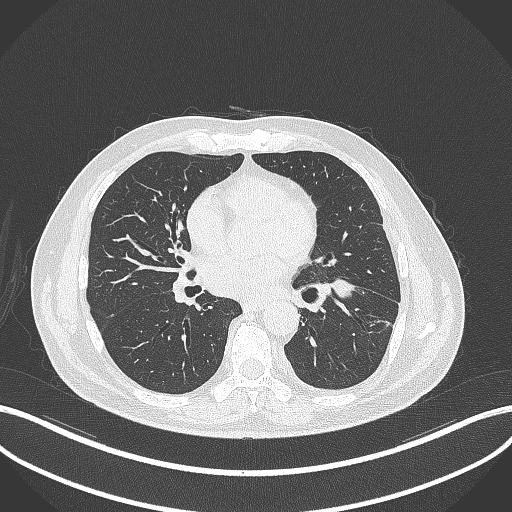
Chest CT, one axial slice. Position 172 of 230 along the scan axis. Reconstruction kernel B70f. 120 kVp. Lung window (W 1500 / L -600 HU). 1 mm slice thickness. 512 × 512 image matrix, field of view 400 × 400 mm. Patient: male, 68 years. Case-level facts recorded for this patient, not image findings: clinical TNM (as recorded): T2b N0 M0.
Structures marked on this image (bounding box drawn by a radiologist):
- lung tumour (recorded histology: squamous cell carcinoma): bounding box [x1, y1, x2, y2] px = [324, 269, 359, 303]